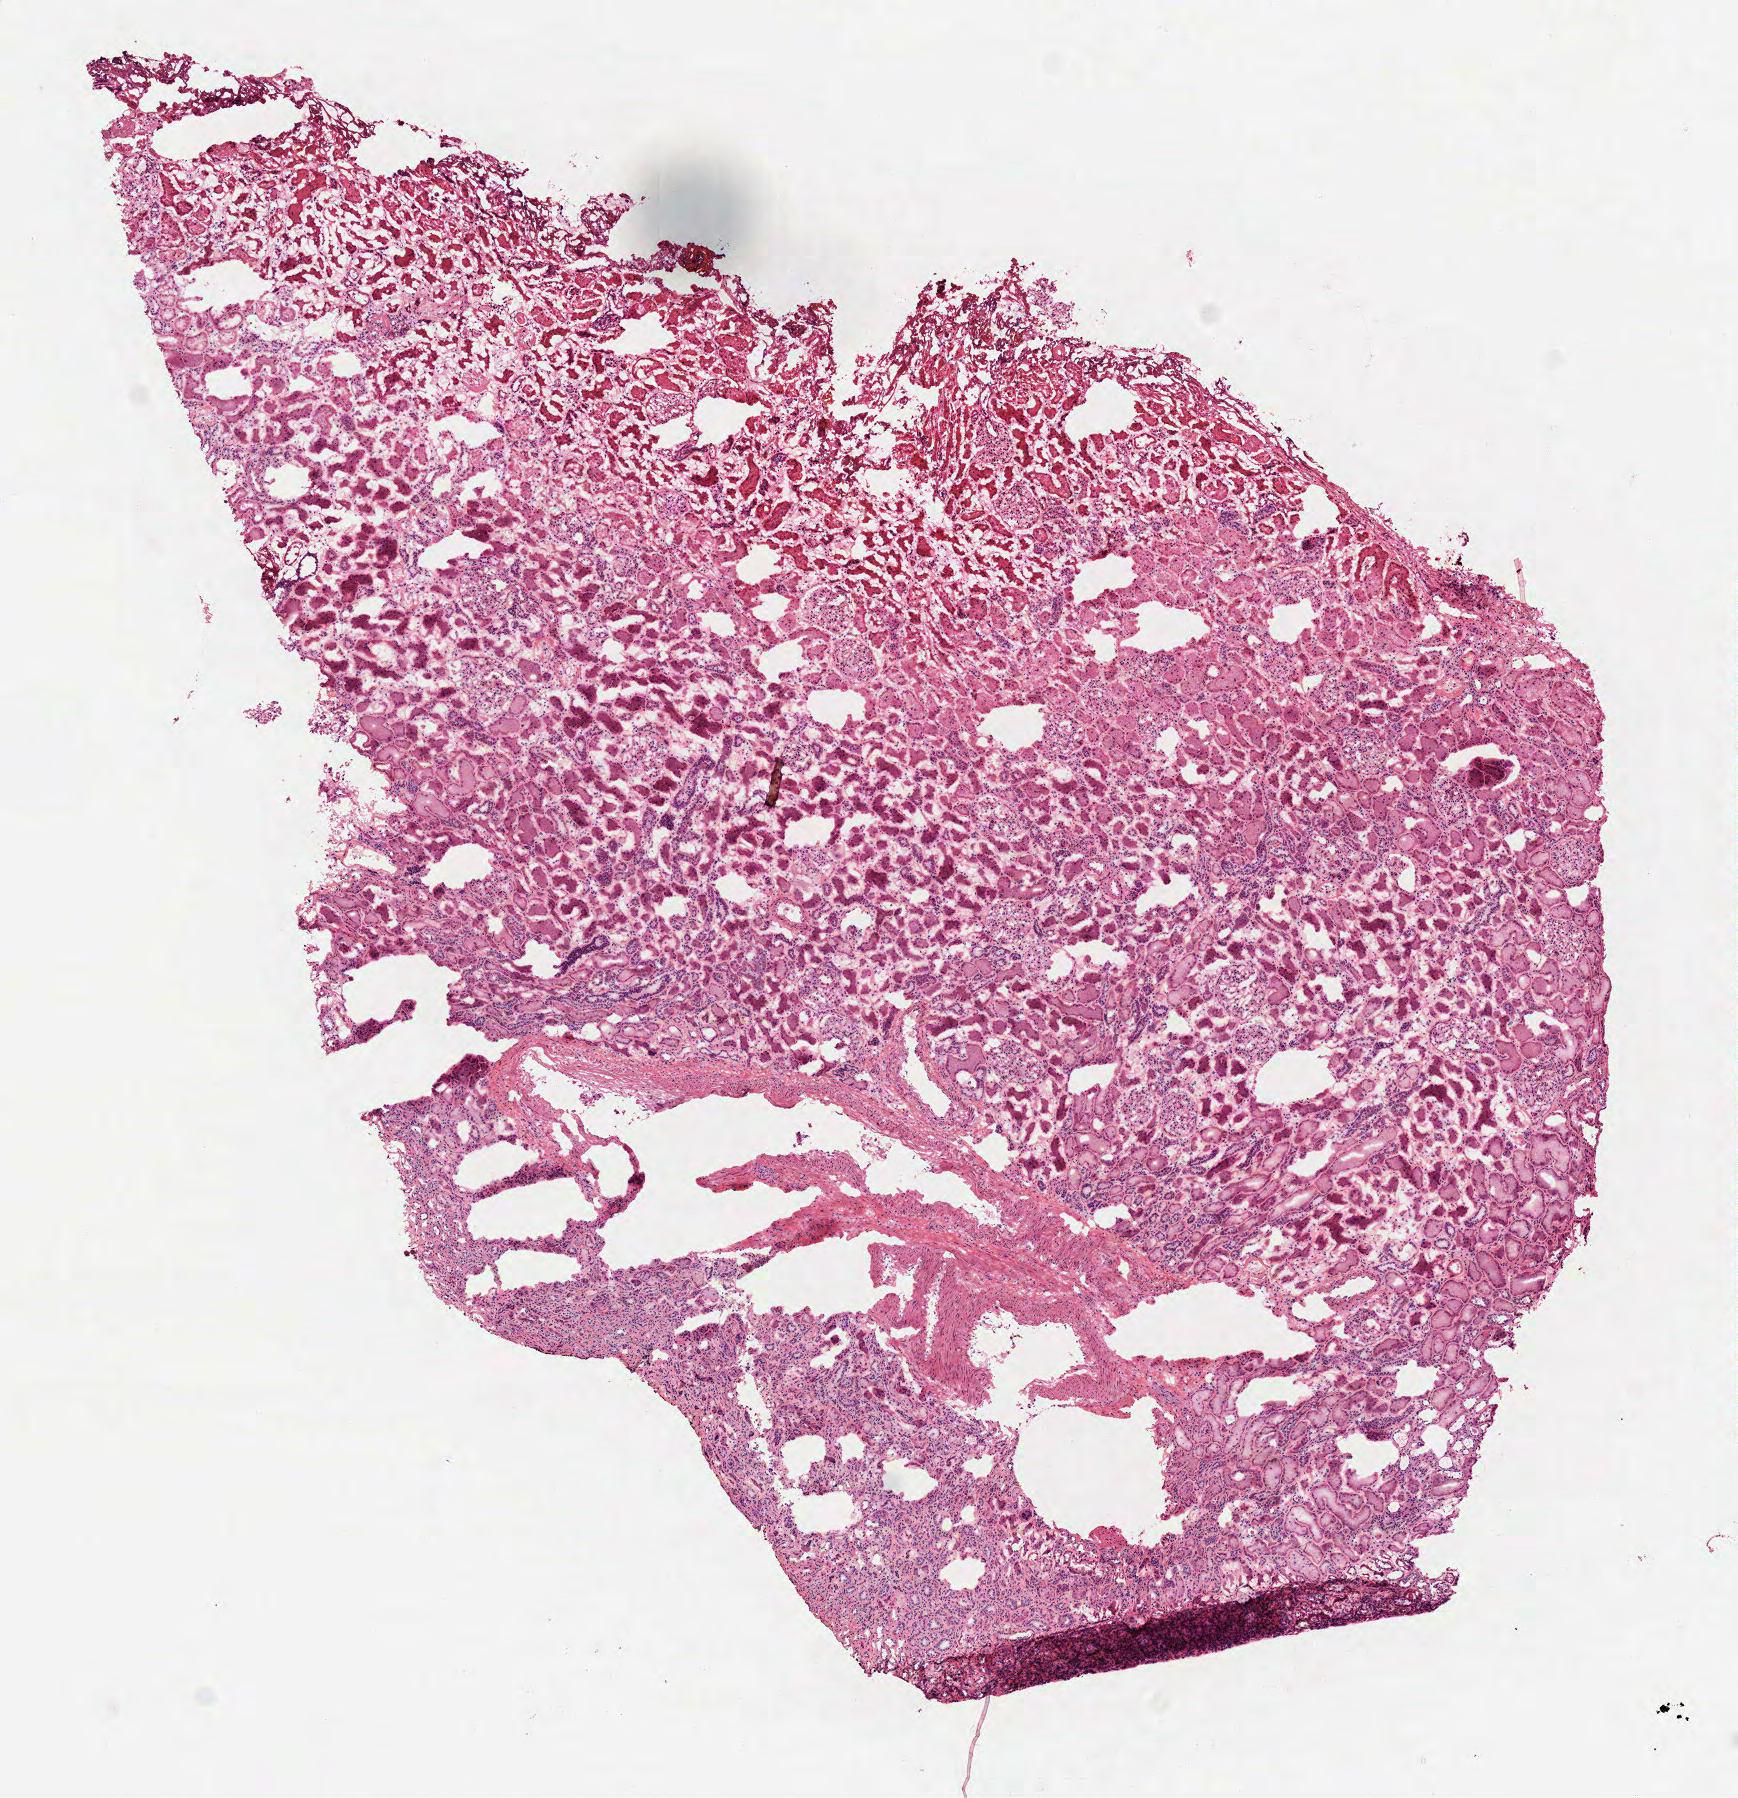
Whole-slide histology image, Hematoxylin and eosin (H&E) stained — low-resolution overview of the scanned area, about 7.0 x 7.3 mm (slide scanned at 40x); frozen section from the top of the tissue portion; kidney, solid tissue normal (non-tumour tissue) sample. Male patient; age at initial diagnosis 53 years.
This section: solid tissue normal sample (biorepository sample class). Patient diagnosis: Papillary adenocarcinoma, NOS.